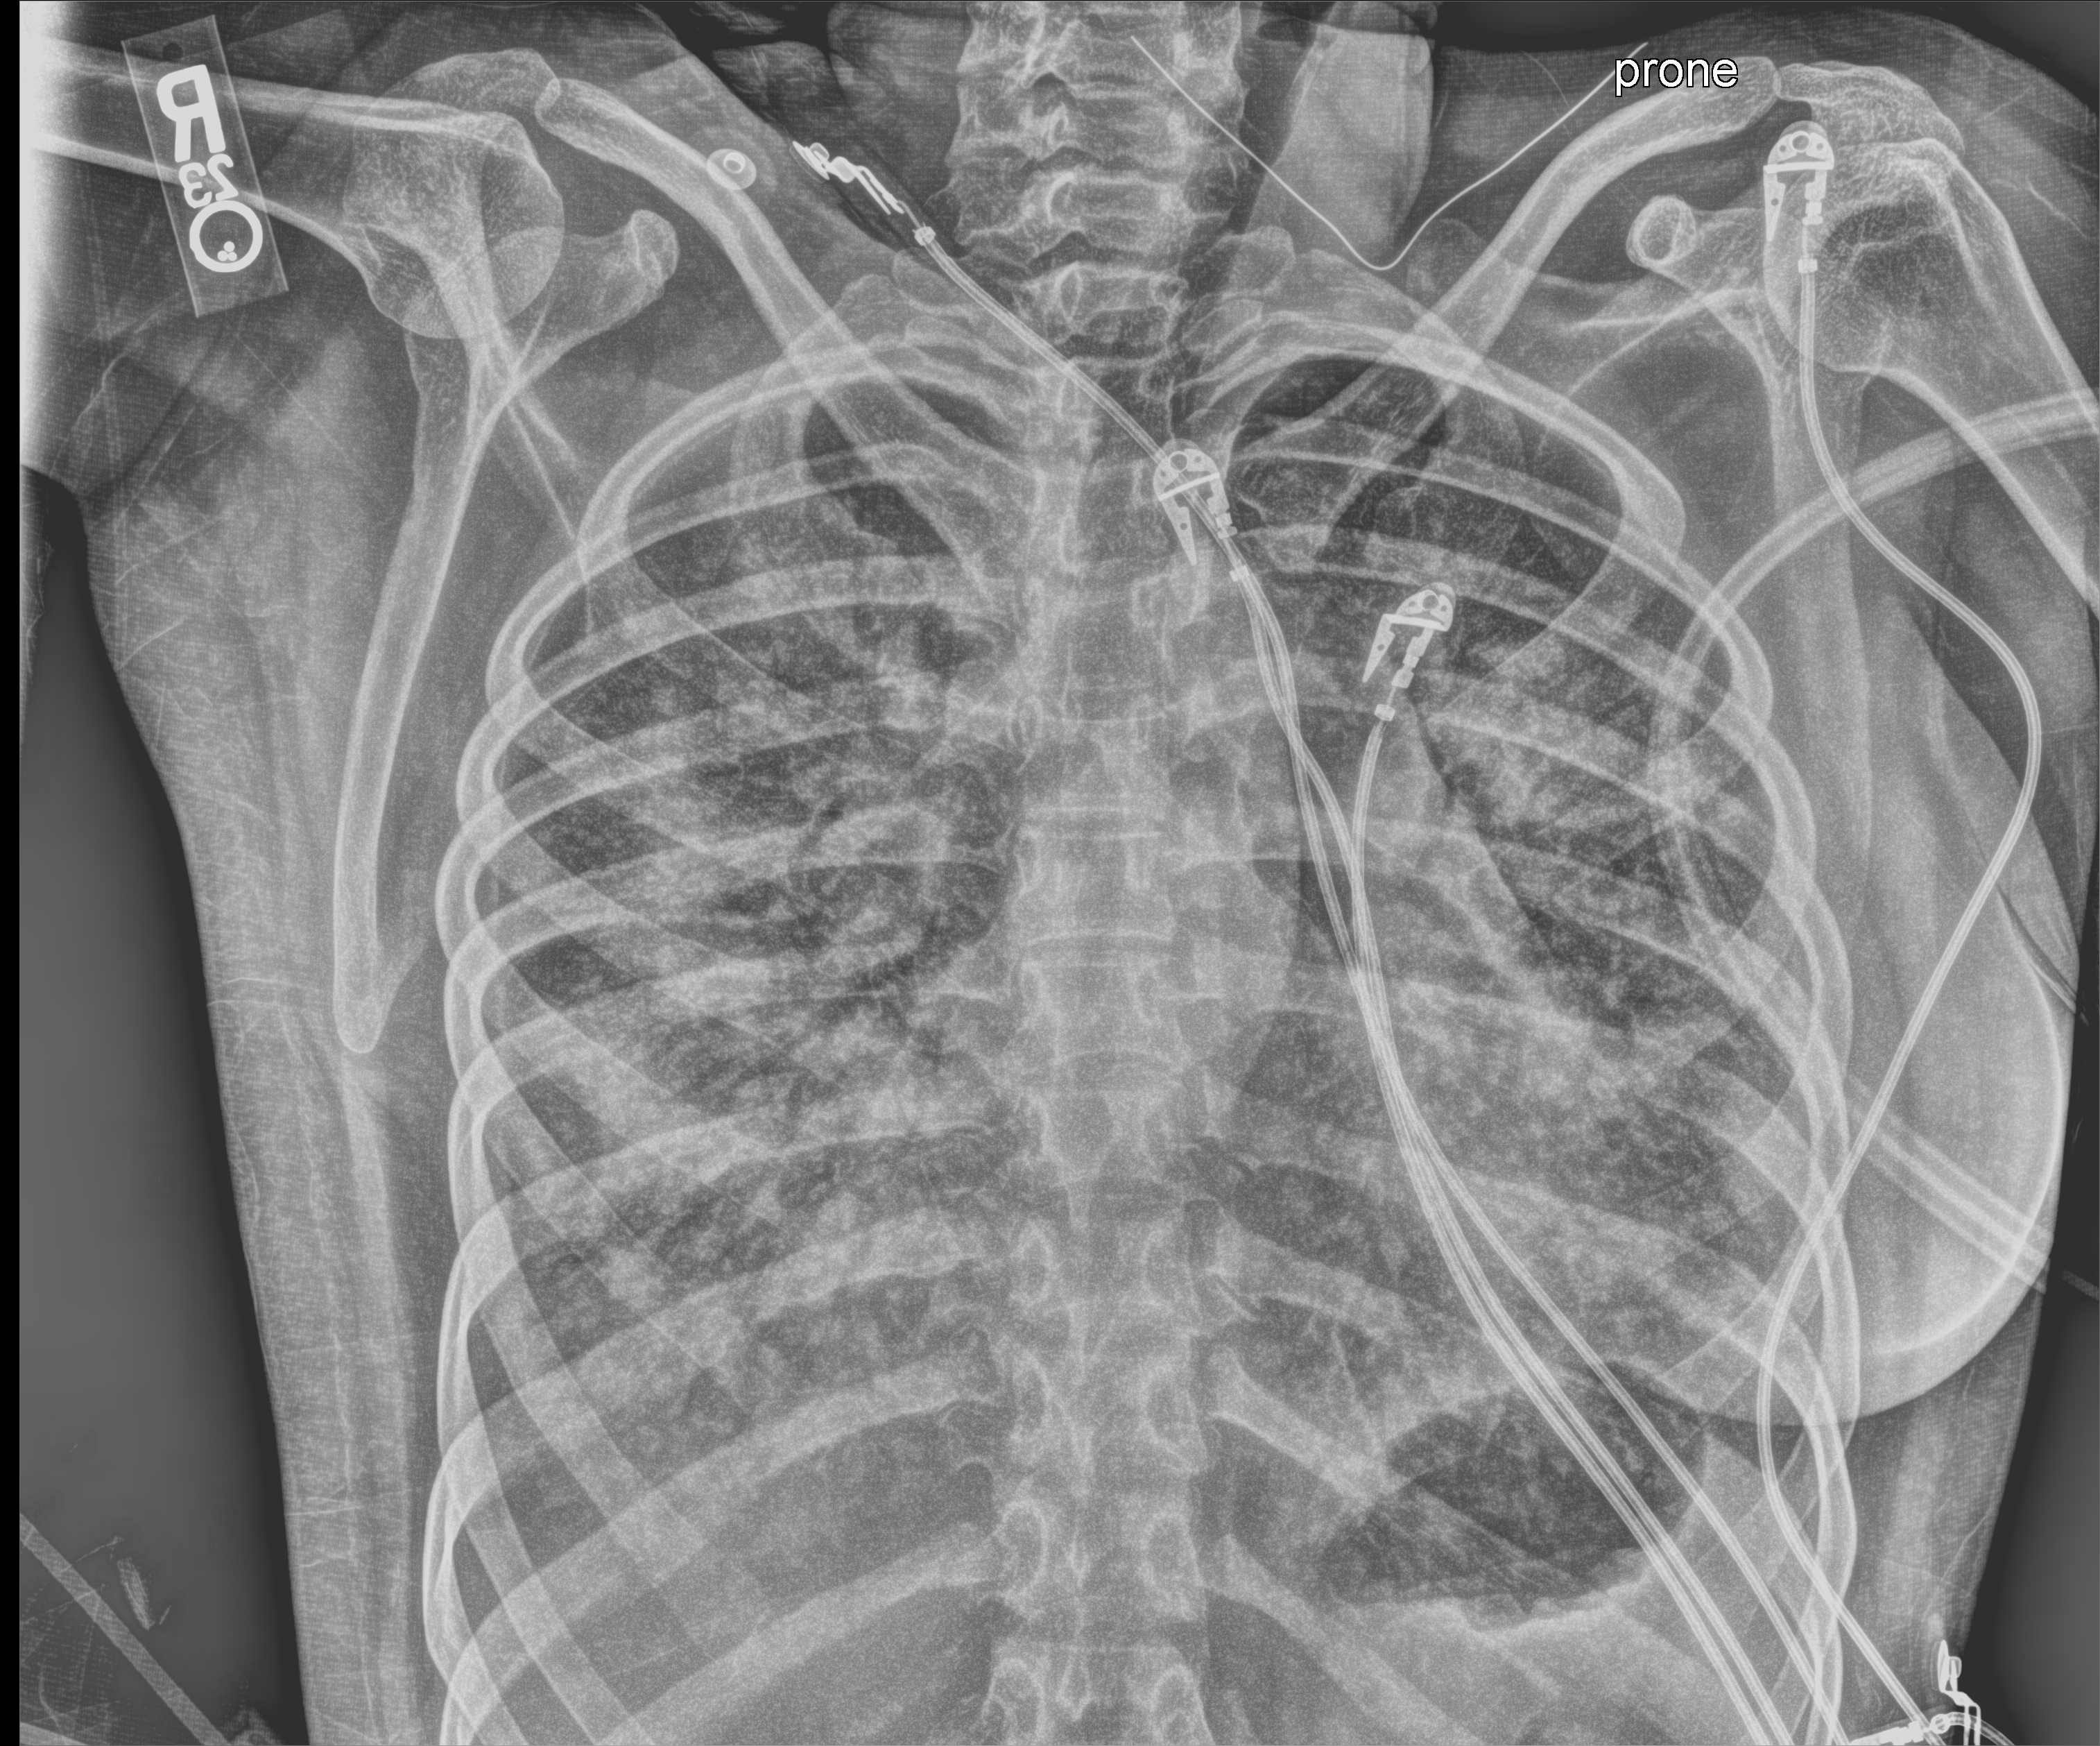
Bedside chest radiograph (computed radiography); anteroposterior (AP) projection. Adult patient hospitalised with COVID-19, age 18–59 years.
Admission-level facts for this patient (not findings on this image; timing relative to this image not recorded): other chronic lung disease (admission record): no.